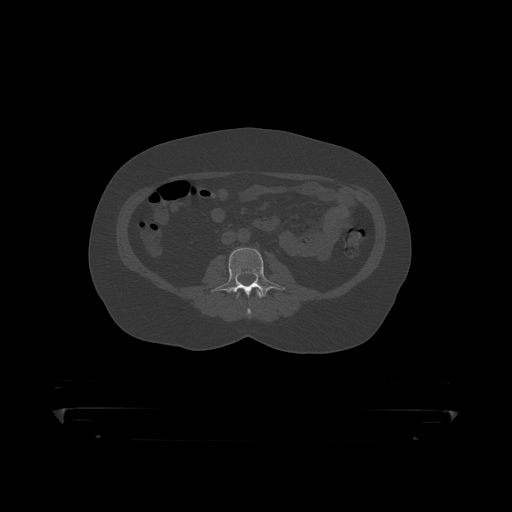
CT including the spine, one axial slice; position 93 of 390 along the scan axis; 120 kVp; bone window (W 1800 / L 400 HU); 512 × 512 image matrix. Patient: male, 60 years. From the clinical record (not read from this slice): primary cancer: prostate.
Outlined on this slice (semi-automatic segmentation, software-assisted and operator-edited):
- L2 vertebra: bounding box <236,290,263,317> (left, top, right, bottom; pixels)
- L3 vertebra: <210,248,285,299>